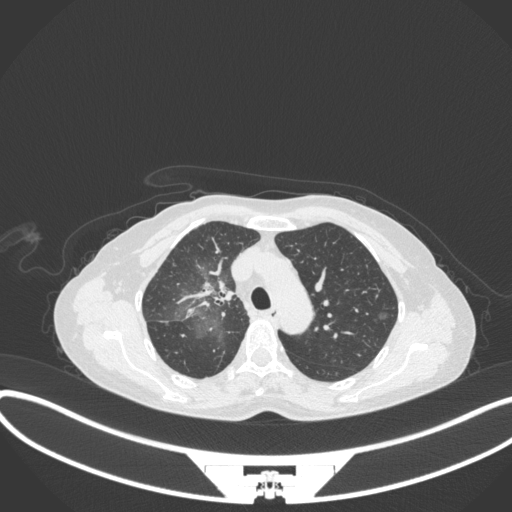
Chest CT, one axial slice. Slice 228 of 311 in the series (ordered by position). Lung window (W 1500 / L -600 HU). 1 mm slice thickness. 512 × 512 image matrix, field of view 400 × 400 mm. Female patient, age 59 years. Case-level facts recorded for this patient, not image findings: clinical TNM (as recorded): T3 N0 M0; histopathological grade: G1.
Annotated regions visible in this slice (bounding box drawn by a radiologist):
- lung tumour (recorded histology: adenocarcinoma): bounding box [x1, y1, x2, y2] px = [192, 278, 232, 311]